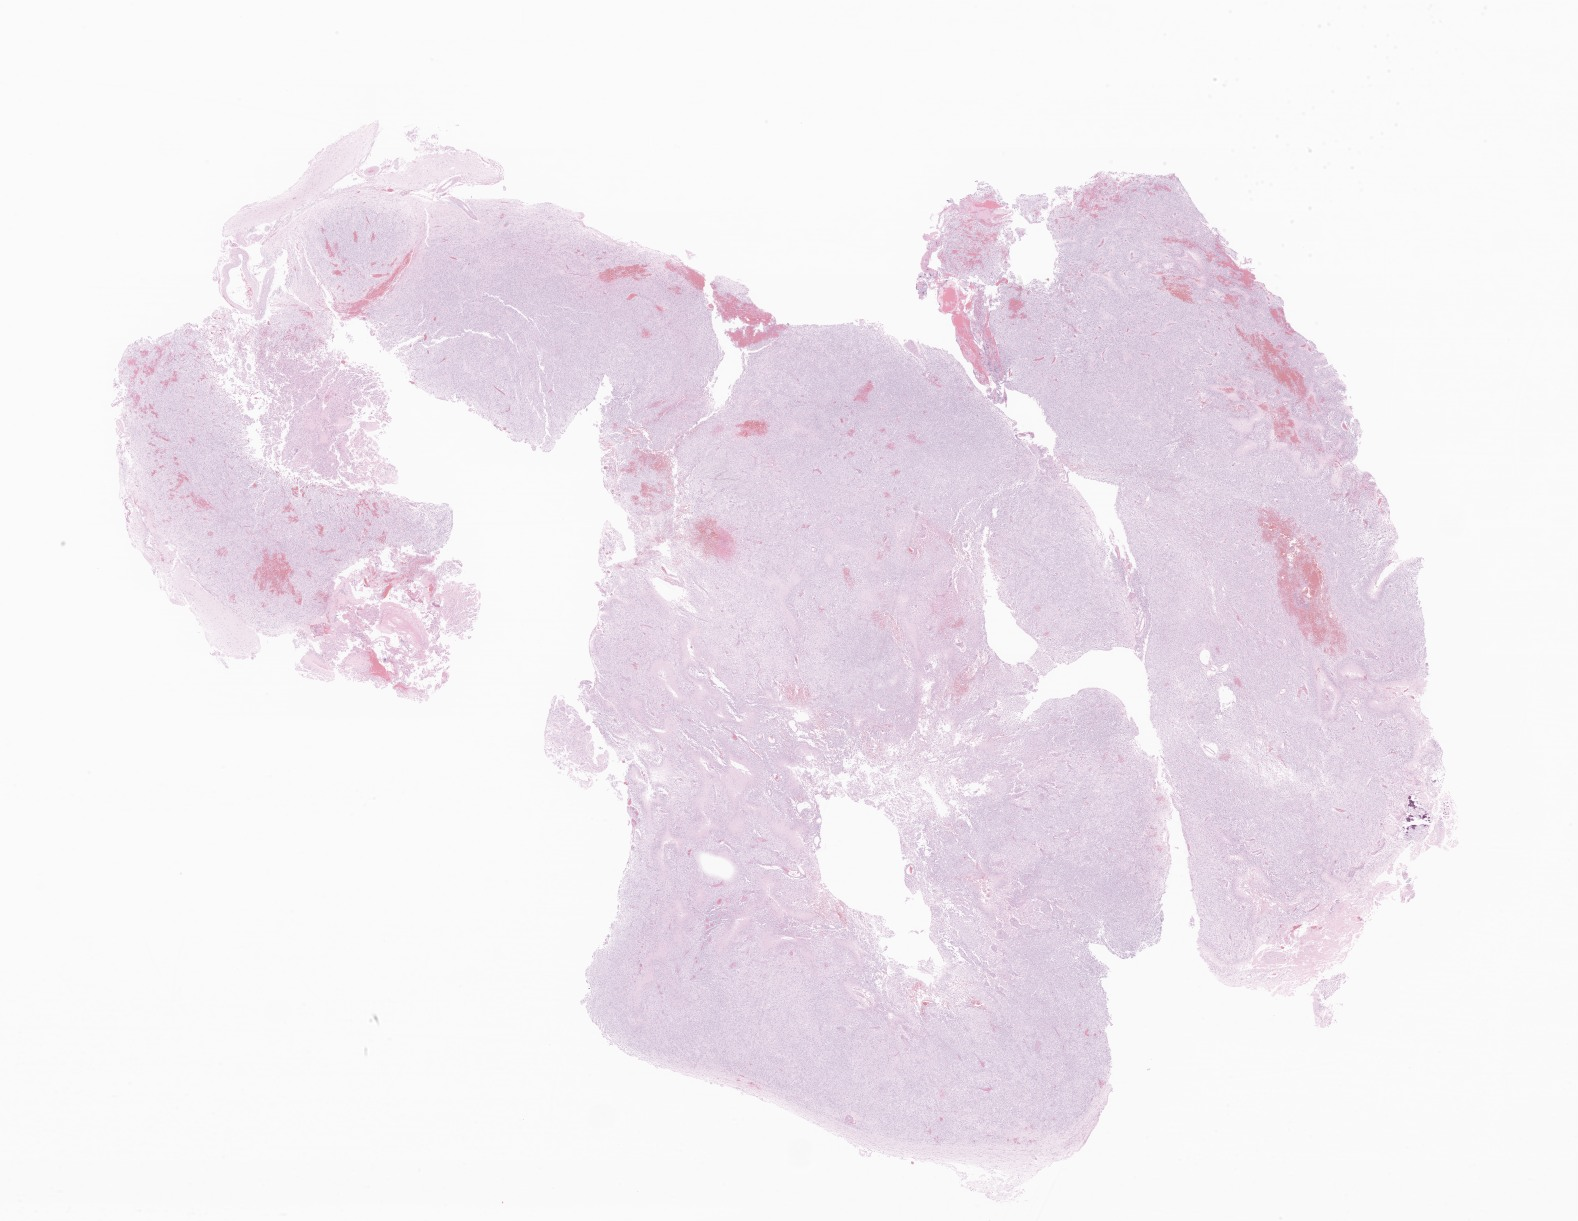
Haematoxylin and eosin whole-slide image of tumor tissue from the brain — shown as a low-resolution overview of the whole scanned area (about 26.6 x 20.6 mm); FFPE section. Patient male; age 92 months (7 years 8 months).
Recorded diagnosis: Neoplasm, malignant.